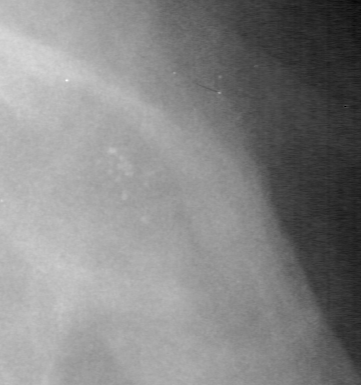
Region of interest cut from a scanned film mammogram (one marked finding), right breast, MLO view.
- Marked abnormality: calcifications, morphology pleomorphic, distribution clustered; BI-RADS assessment category 4; pathology result (as recorded, not read from the image): benign.